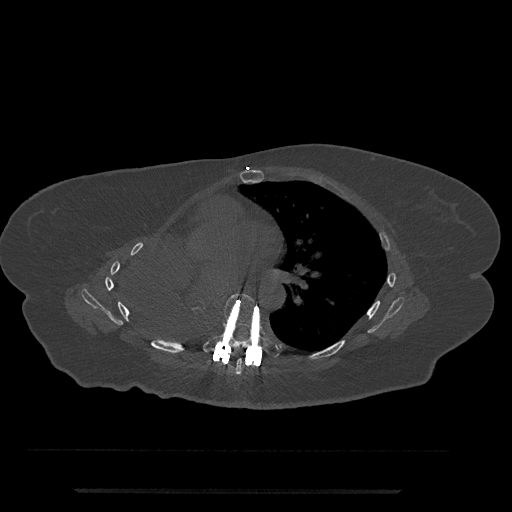
CT including the spine, one axial slice. Position 454 of 797 along the scan axis. Reconstruction kernel Br40s/3. Bone window (W 1800 / L 400 HU). 512 × 512 image matrix, field of view 440 × 440 mm. Female patient, age 51 years. From the clinical record (not read from this slice): primary cancer: neuro.
Outlined on this slice (semi-automatically segmented with operator editing):
- T6 vertebra: bounding box [x1, y1, x2, y2] px = [235, 358, 242, 375]
- T7 vertebra: [203, 293, 281, 358]